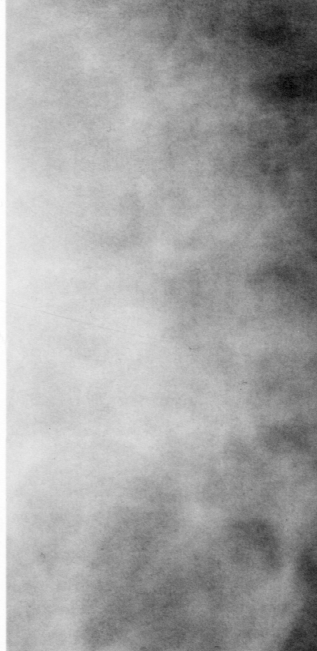
Cropped region of a digitized screen-film mammogram centred on a radiologist-marked abnormality, left breast, CC view.
Mass, shape asymmetric breast tissue, margins ill defined; BI-RADS assessment category 5; pathology result (as recorded, not read from the image): malignant.